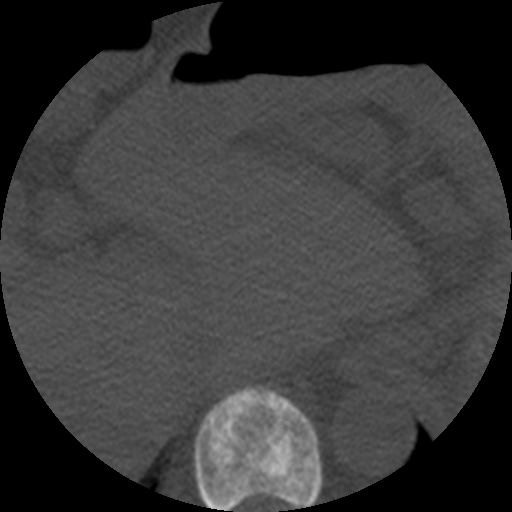
CT including the spine, one axial slice. Position 262 of 508 along the scan axis. Reconstruction kernel STANDARD. 120 kVp. Bone window (W 1800 / L 400 HU). 512 × 512 image matrix, field of view 160 × 160 mm. Patient age 57 years. From the clinical record (not read from this slice): primary cancer: prostate.
Annotated regions visible in this slice (semi-automatically segmented with operator editing):
- T10 vertebra: bounding box (x1, y1, x2, y2) in pixels: (194, 386, 323, 512)